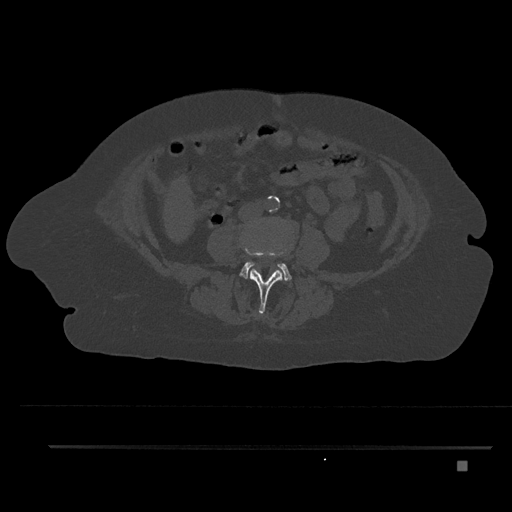
CT including the spine, one axial slice. 120 kVp. Bone window (W 1800 / L 400 HU). 512 × 512 image matrix, field of view 437 × 437 mm. Patient: female, 76 years. From the clinical record (not read from this slice): primary cancer: lung.
Annotated regions visible in this slice (semi-automatic segmentation, software-assisted and operator-edited):
- L3 vertebra: box from (x=242, y=232) to (x=292, y=313) px
- L4 vertebra: (x=241, y=238)–(x=291, y=281)